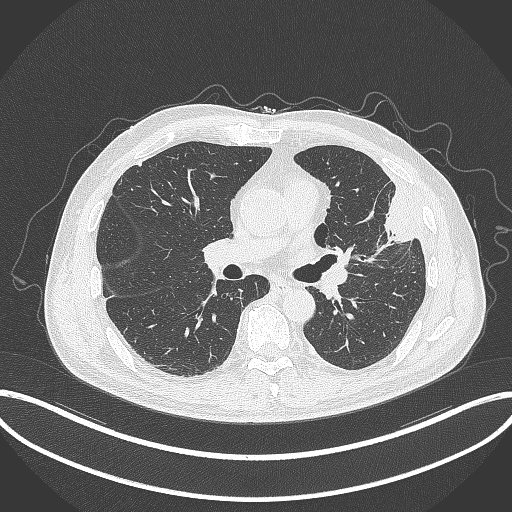
Chest CT, one axial slice; position 183 of 382 along the scan axis; lung window (W 1500 / L -600 HU); 512 × 512 image matrix, field of view 415 × 415 mm. Male patient, age 64 years. Case-level facts recorded for this patient, not image findings: clinical TNM (as recorded): T4 N1 M0; histopathological grade: G3.
Outlined on this slice (bounding box drawn by a radiologist):
- lung tumour (recorded histology: adenocarcinoma): bounding box <371,191,426,252> (left, top, right, bottom; pixels)